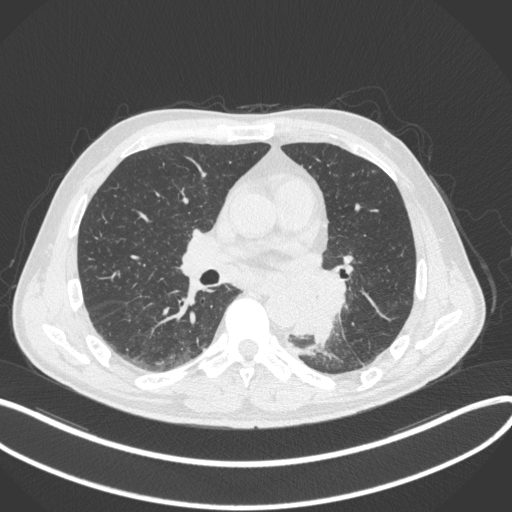
Chest CT, one axial slice; position 174 of 328 along the scan axis; lung window (W 1500 / L -600 HU); 1 mm slice thickness; 512 × 512 image matrix, field of view 400 × 400 mm. Male patient, age 59 years. From the clinical record (not read from this slice): clinical TNM (as recorded): T2a N2 M0.
Outlined on this slice (bounding box drawn by a radiologist):
- lung tumour (recorded histology: squamous cell carcinoma): bounding box (x1, y1, x2, y2) in pixels: (286, 265, 349, 344)